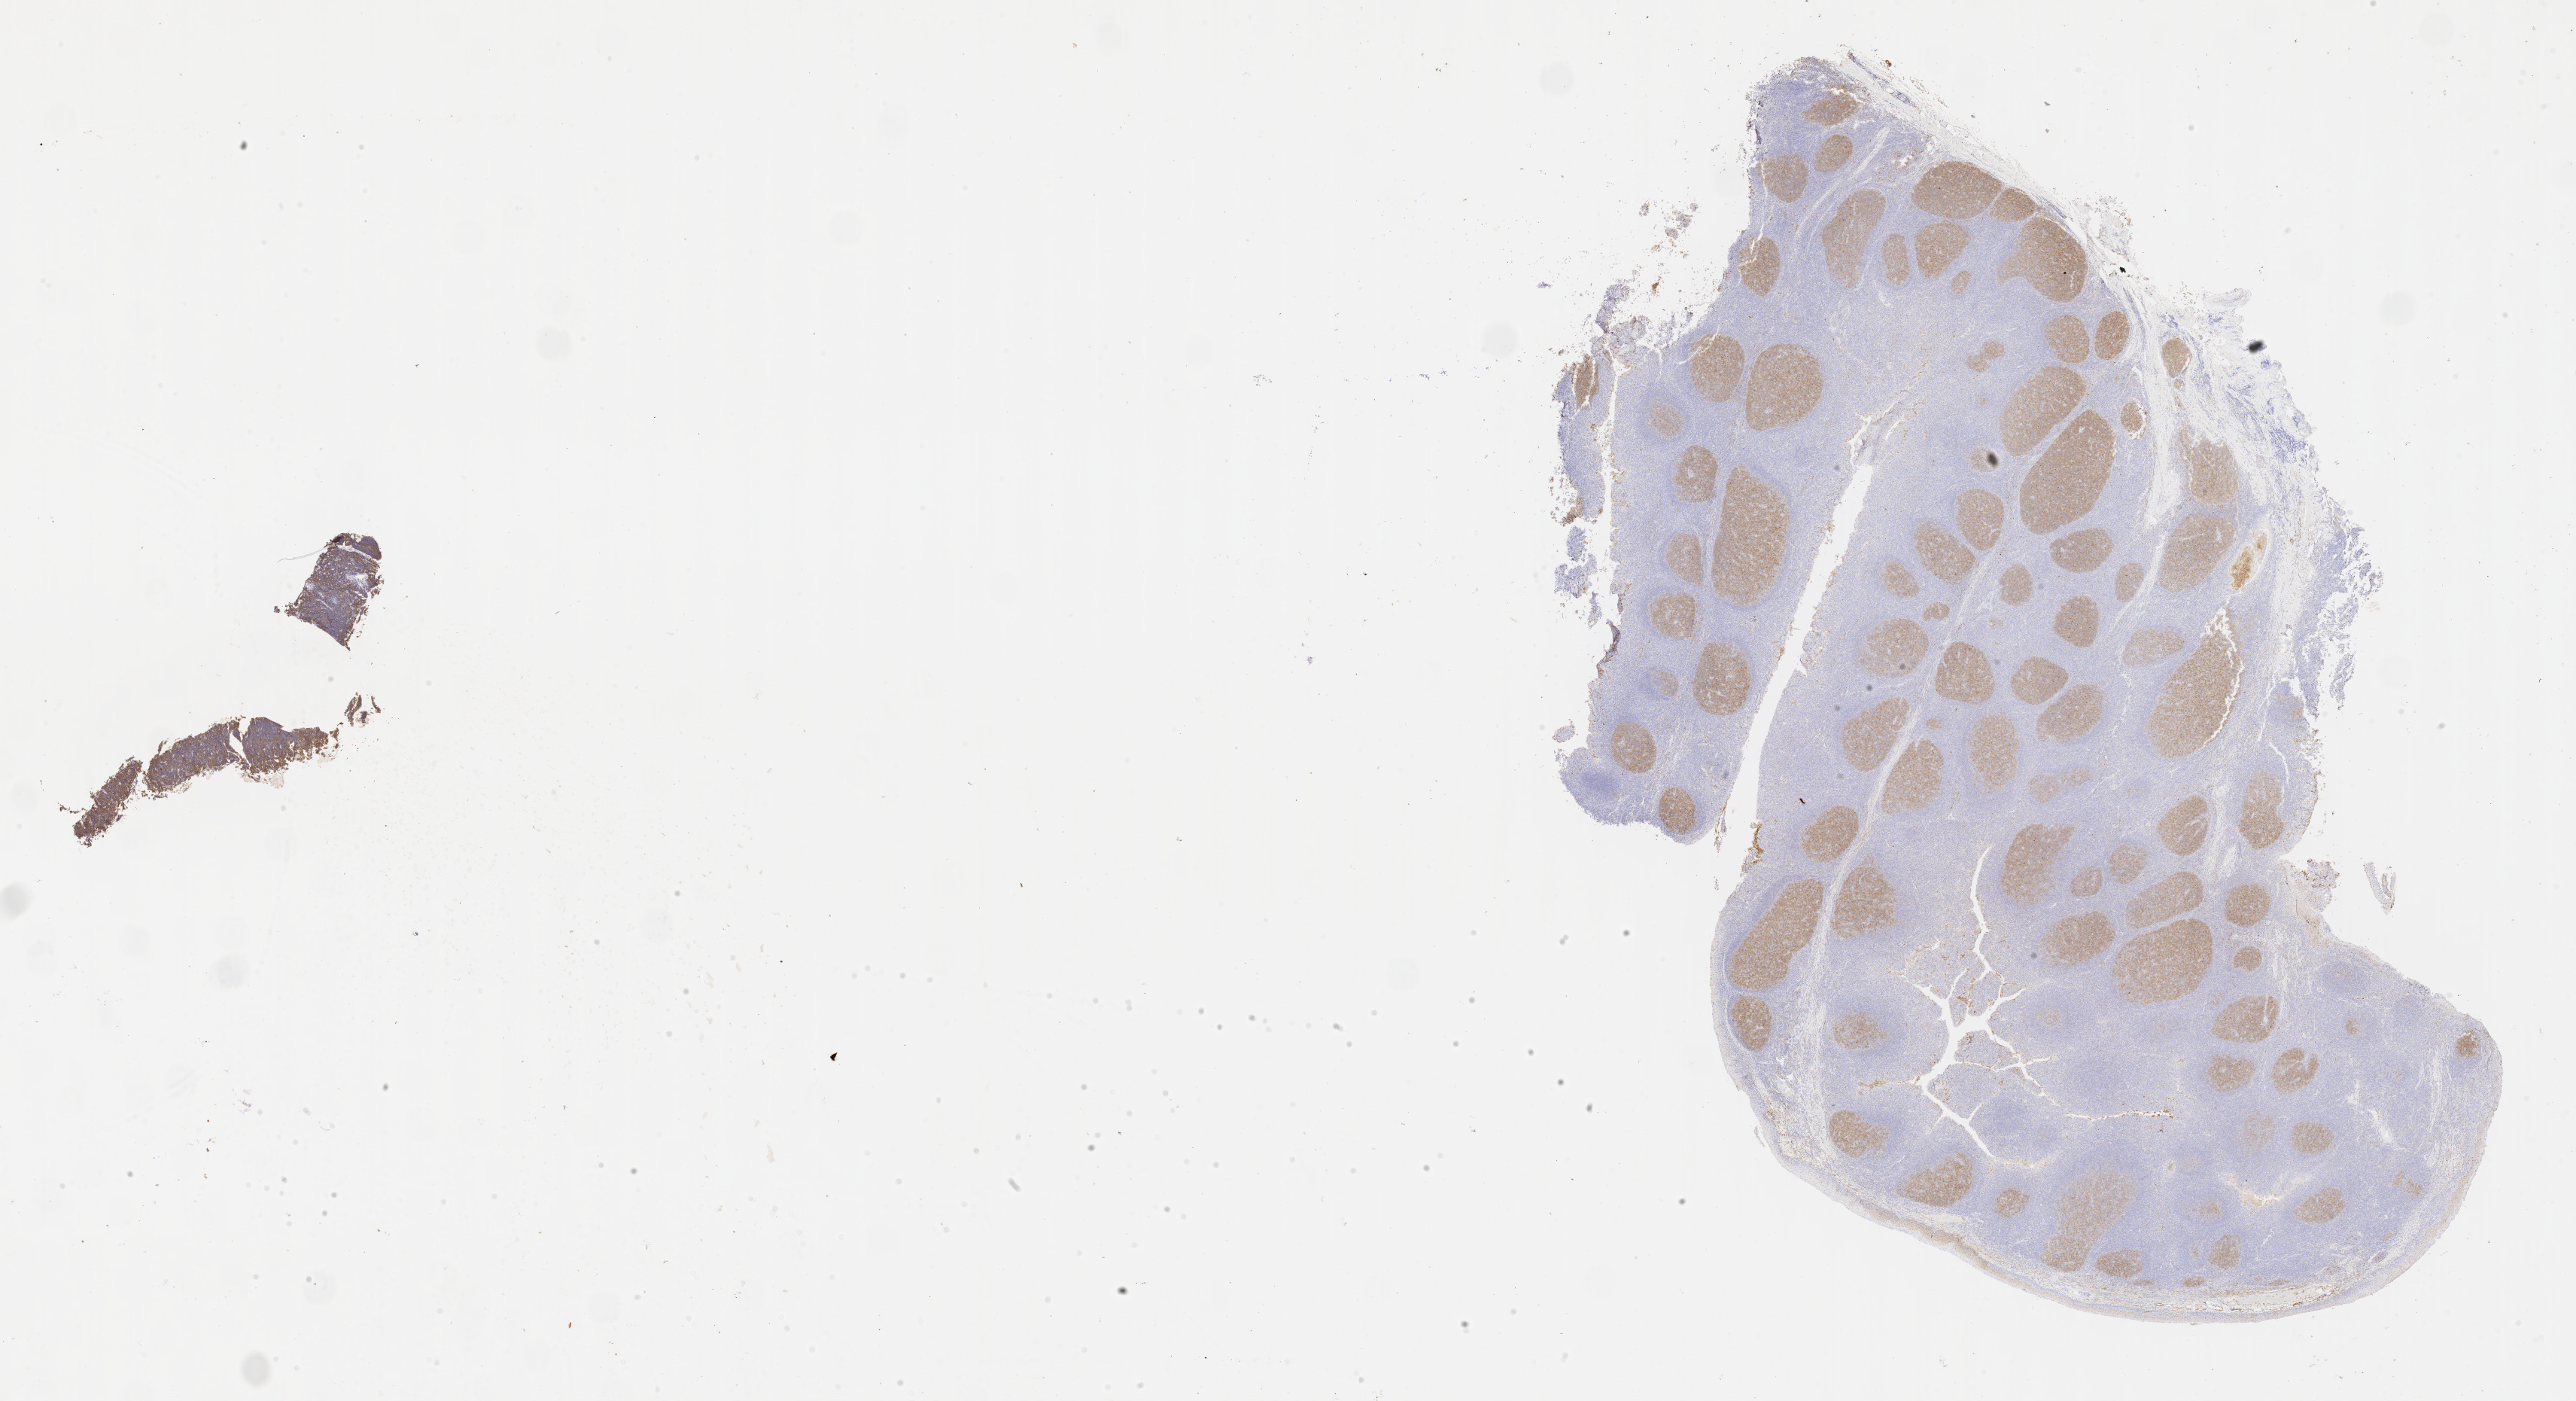
Whole-slide image, immunohistochemical stain for CD10 — whole scanned area (about 27.7 x 15.0 mm) shown as a low-resolution overview, specimen: tumor tissue, site: cranium. Patient: male, age at initial diagnosis 6 years.
• histologic diagnosis: Burkitt lymphoma, NOS